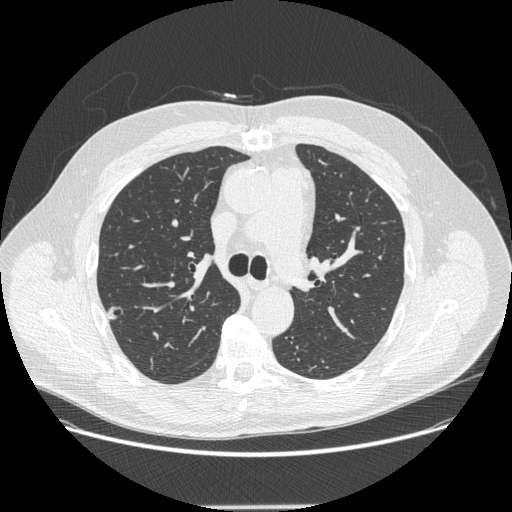
Low-dose screening chest CT, axial slice; third annual screen; lung window (W 1500 / L -600 HU); 120 kVp; 512 × 512 image matrix. Male participant, aged 62 years at enrolment. Current smoker at enrolment.
- Expert reader's lesion annotation, bounding box <94,299,132,331> (left, top, right, bottom; pixels).
- Screening reader's record for this exam (one nodule recorded; not confirmed to be the boxed lesion): non-calcified nodule or mass ≥4 mm, right upper lobe, 12 × 11 mm, smooth margins, soft tissue attenuation, pre-existing on the prior screen: yes; interval growth: yes.
- Later outcome: lung cancer diagnosed 112 days after this screen — adenocarcinoma, NOS, right upper lobe, moderately differentiated (G2), stage IA (AJCC 6th edition), 12 mm at pathology.